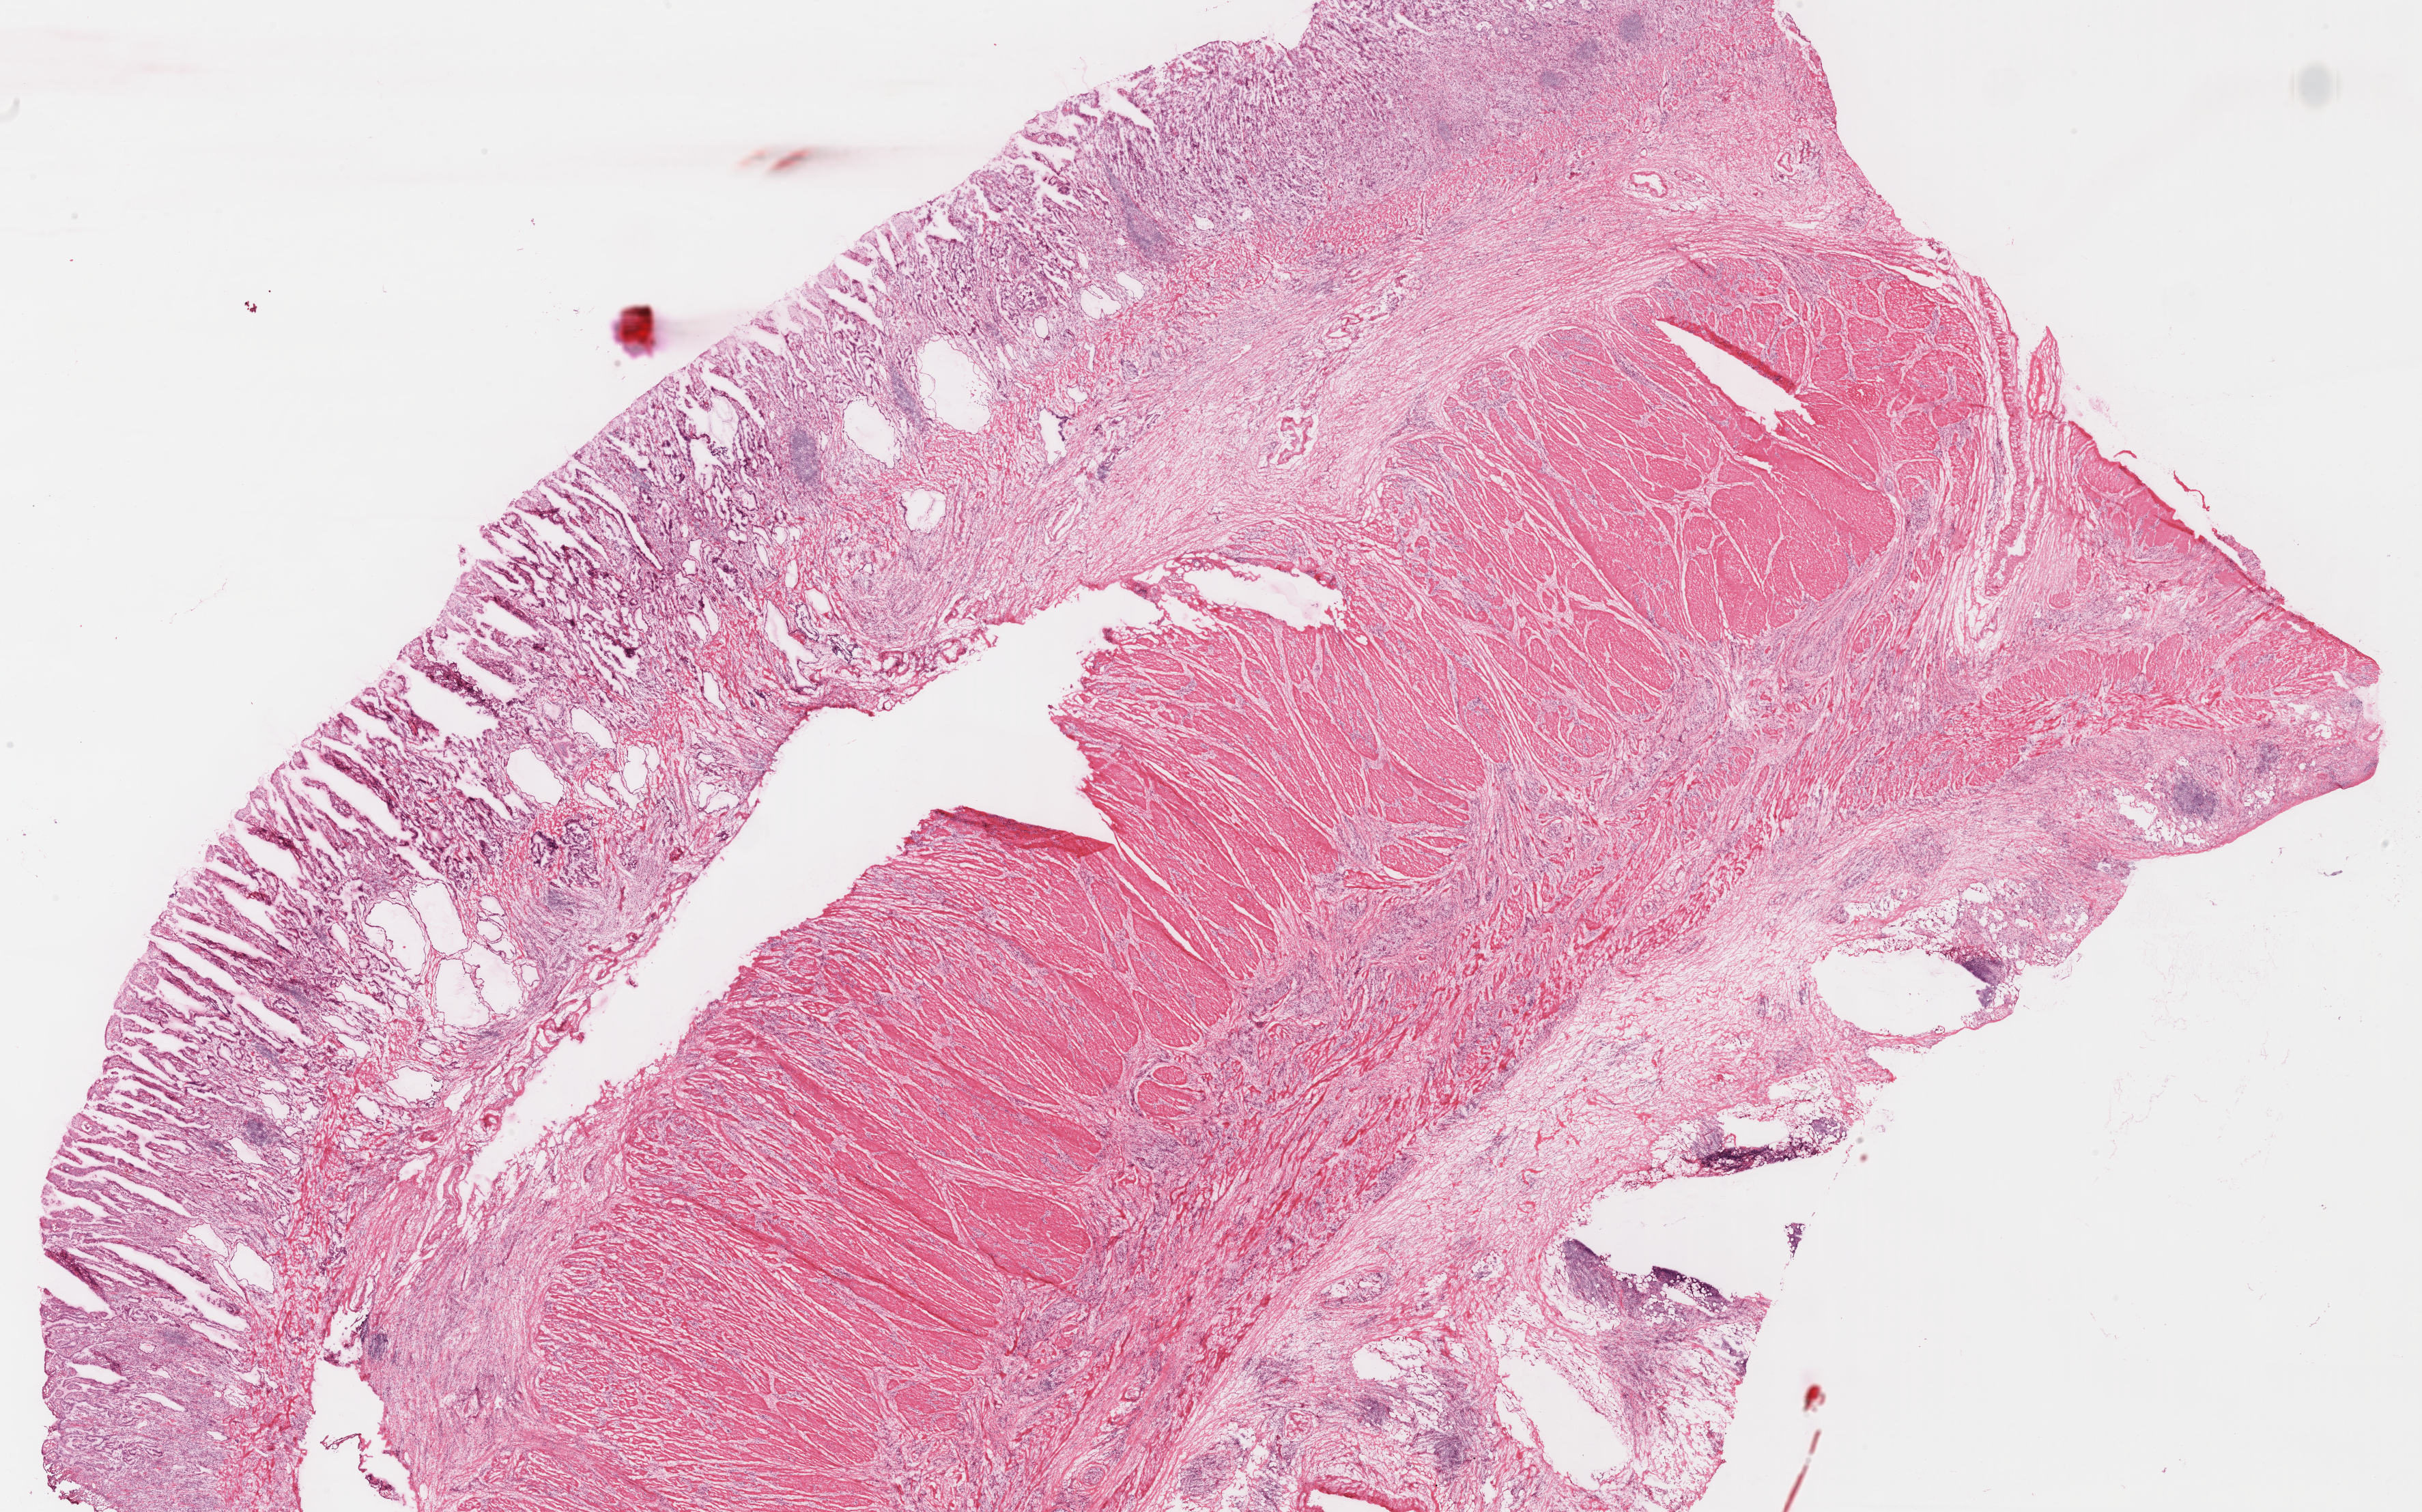
Whole-slide histology image, H&E-stained — shown as a low-resolution overview of the whole scanned area (about 27.9 x 17.4 mm, acquisition: 40x scan). Frozen section from the top of the tissue portion. Primary tumour sample from the stomach. Male, age 58 years at initial diagnosis. Histologic grade: GX (grade cannot be assessed). Pathologist review of this section (percent, as recorded): tumour cells 30%, tumour nuclei 65%, normal cells 0%, stromal cells 70%, necrosis 0%.
• pathologic diagnosis: Carcinoma, diffuse type
• AJCC pathologic stage: IIIC (7th edition)
• lymph nodes positive (case pathology): 11 of 11 examined